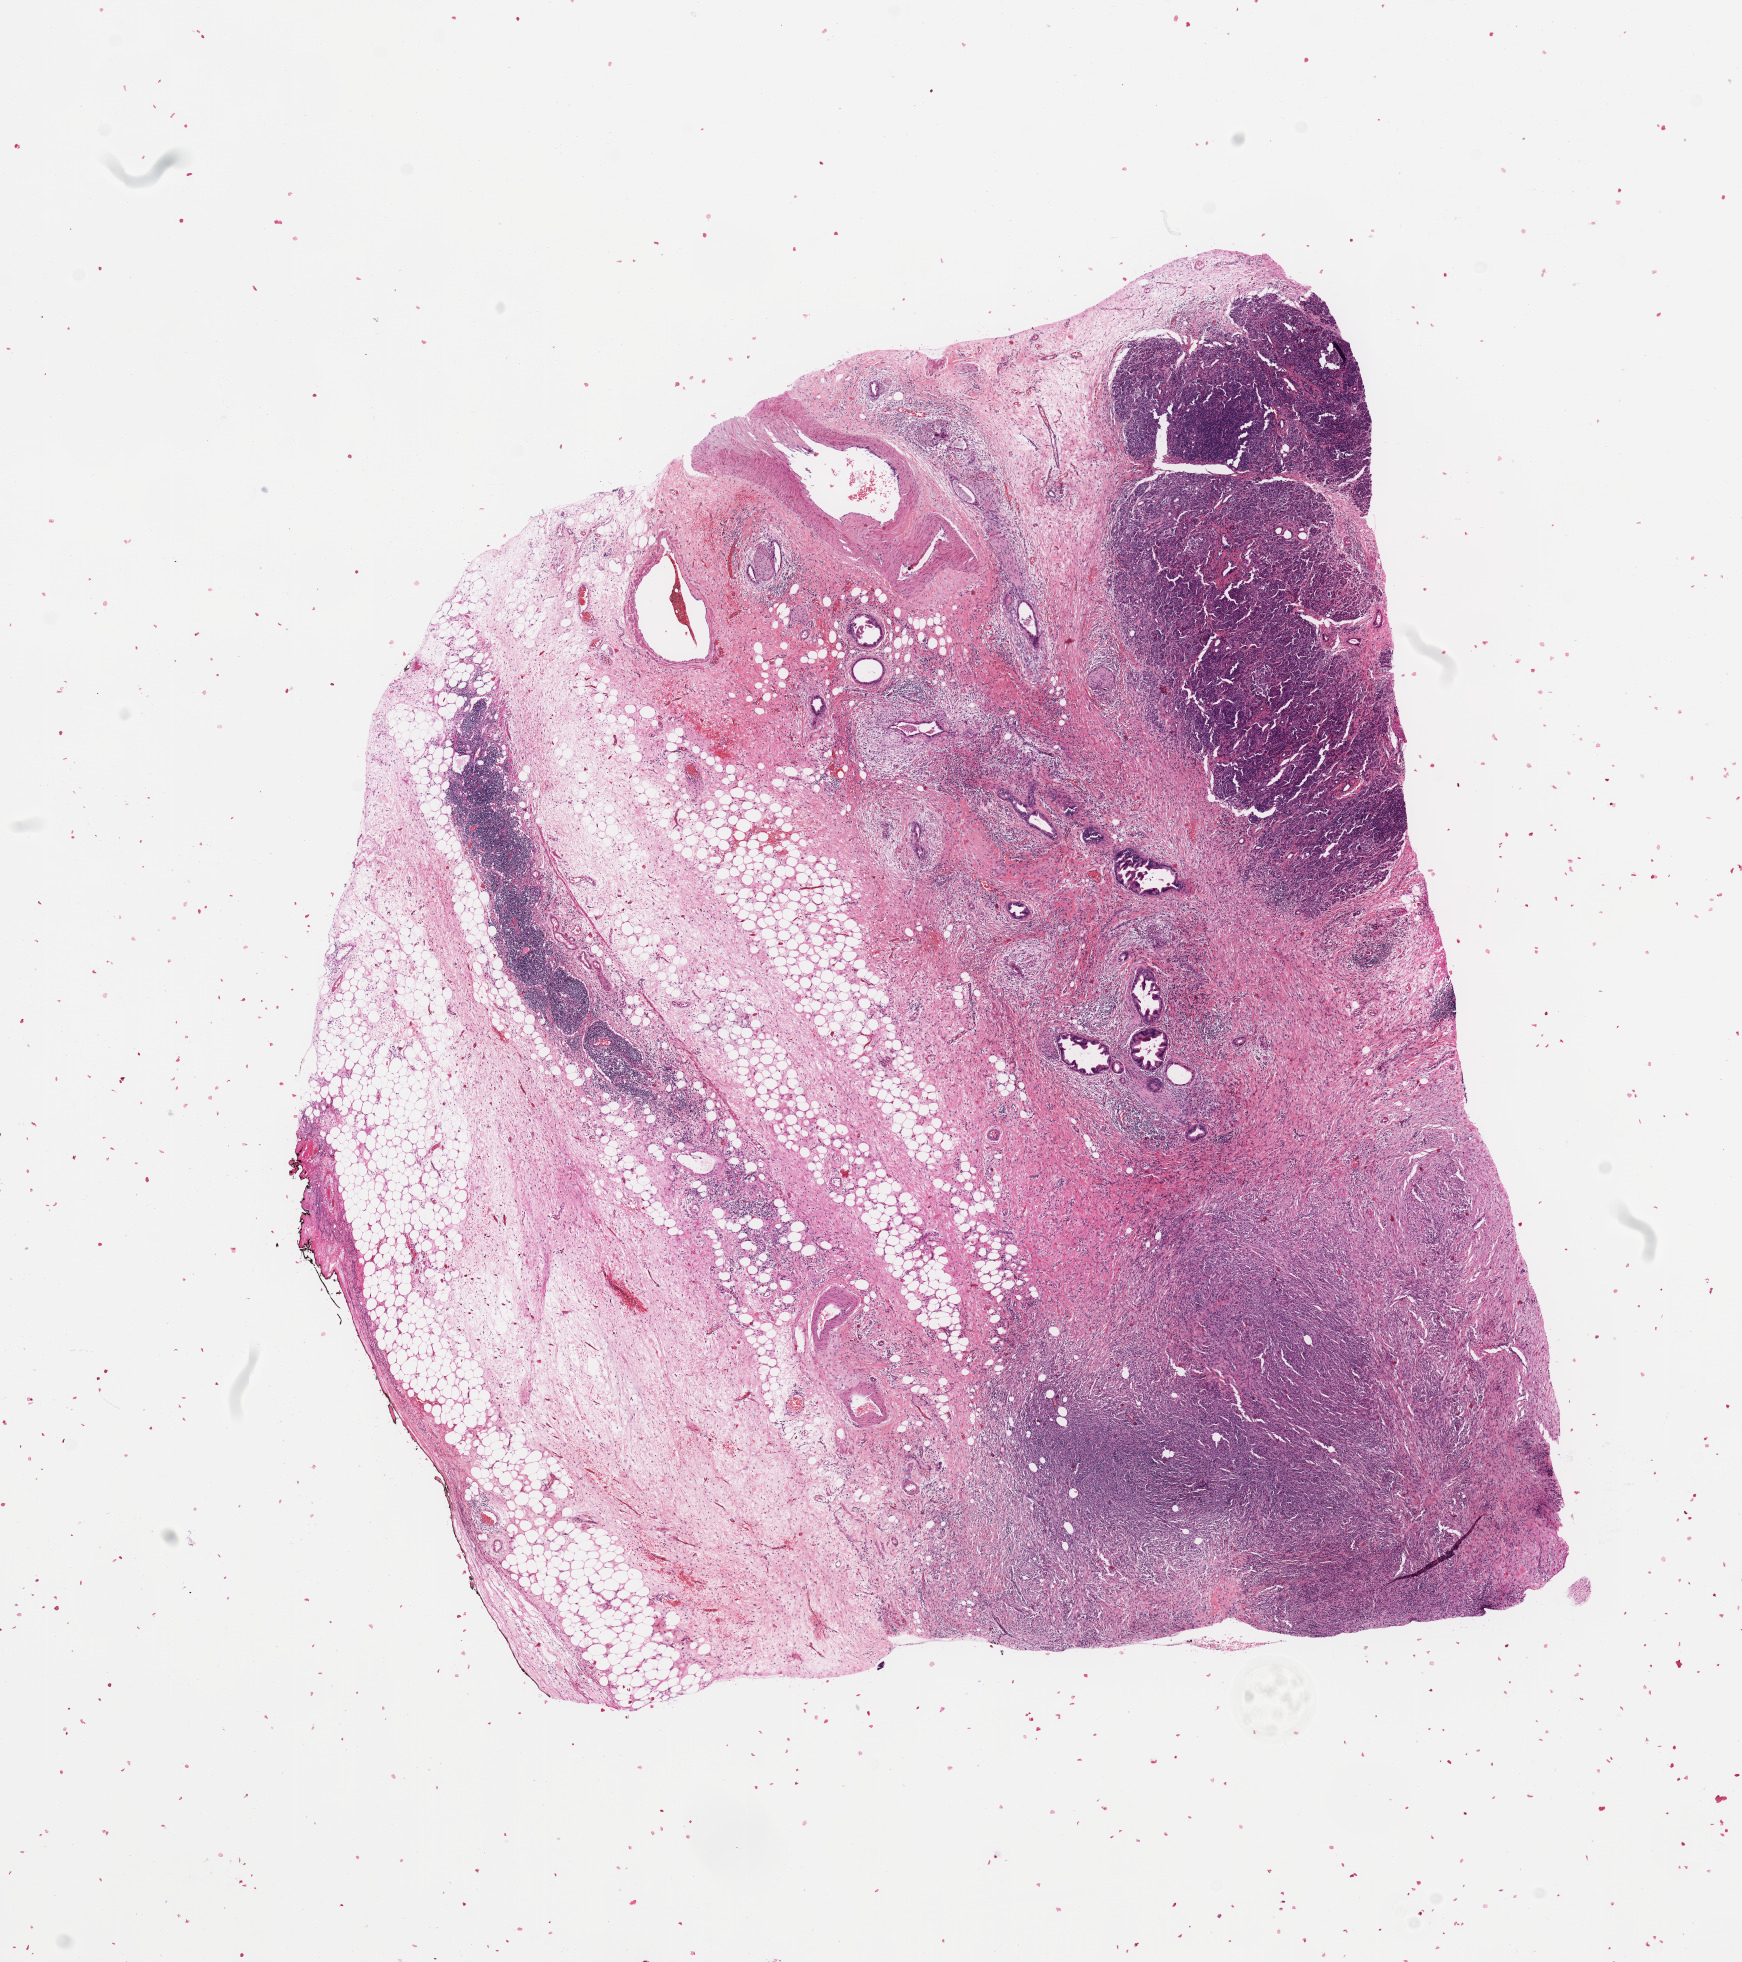
Digitized Hematoxylin and eosin (H&E) stained tissue section (whole slide) — low-resolution overview of the scanned area, about 13.8 x 15.5 mm. Pancreas, tumour tissue. Female, 68 y/o. Histologic grade: G2 (moderately differentiated).
• AJCC pathologic stage: IB
• primary tumour site (as recorded): head
• histologic diagnosis: Infiltrating duct carcinoma, NOS